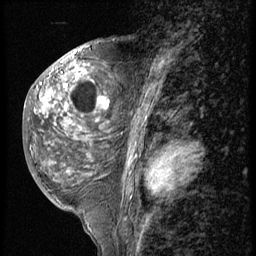
Breast MRI (dynamic contrast-enhanced), one sagittal slice; slice 27 of 56 in the series (ordered by position); 3 images stored at this slice position (order not interpretable as contrast timing); 1.5 T; TE 4.2 ms, TR 9 ms; 256 × 256 image matrix, field of view 180 × 180 mm. Female patient, age 50 years. From the clinical record (not read from this slice): setting: breast cancer imaged before/during neoadjuvant chemotherapy; receptor status: triple-negative.
Annotated regions visible in this slice (semi-automatic segmentation, software-assisted and operator-edited):
- analysis volume of interest (the breast-tissue region the enhancement analysis was run in; not a lesion): bounding box [x1, y1, x2, y2] px = [25, 50, 117, 191]
- tumour enhancement mask (voxels above the 140 % enhancement threshold inside the analysis volume of interest): [40, 66, 109, 111]